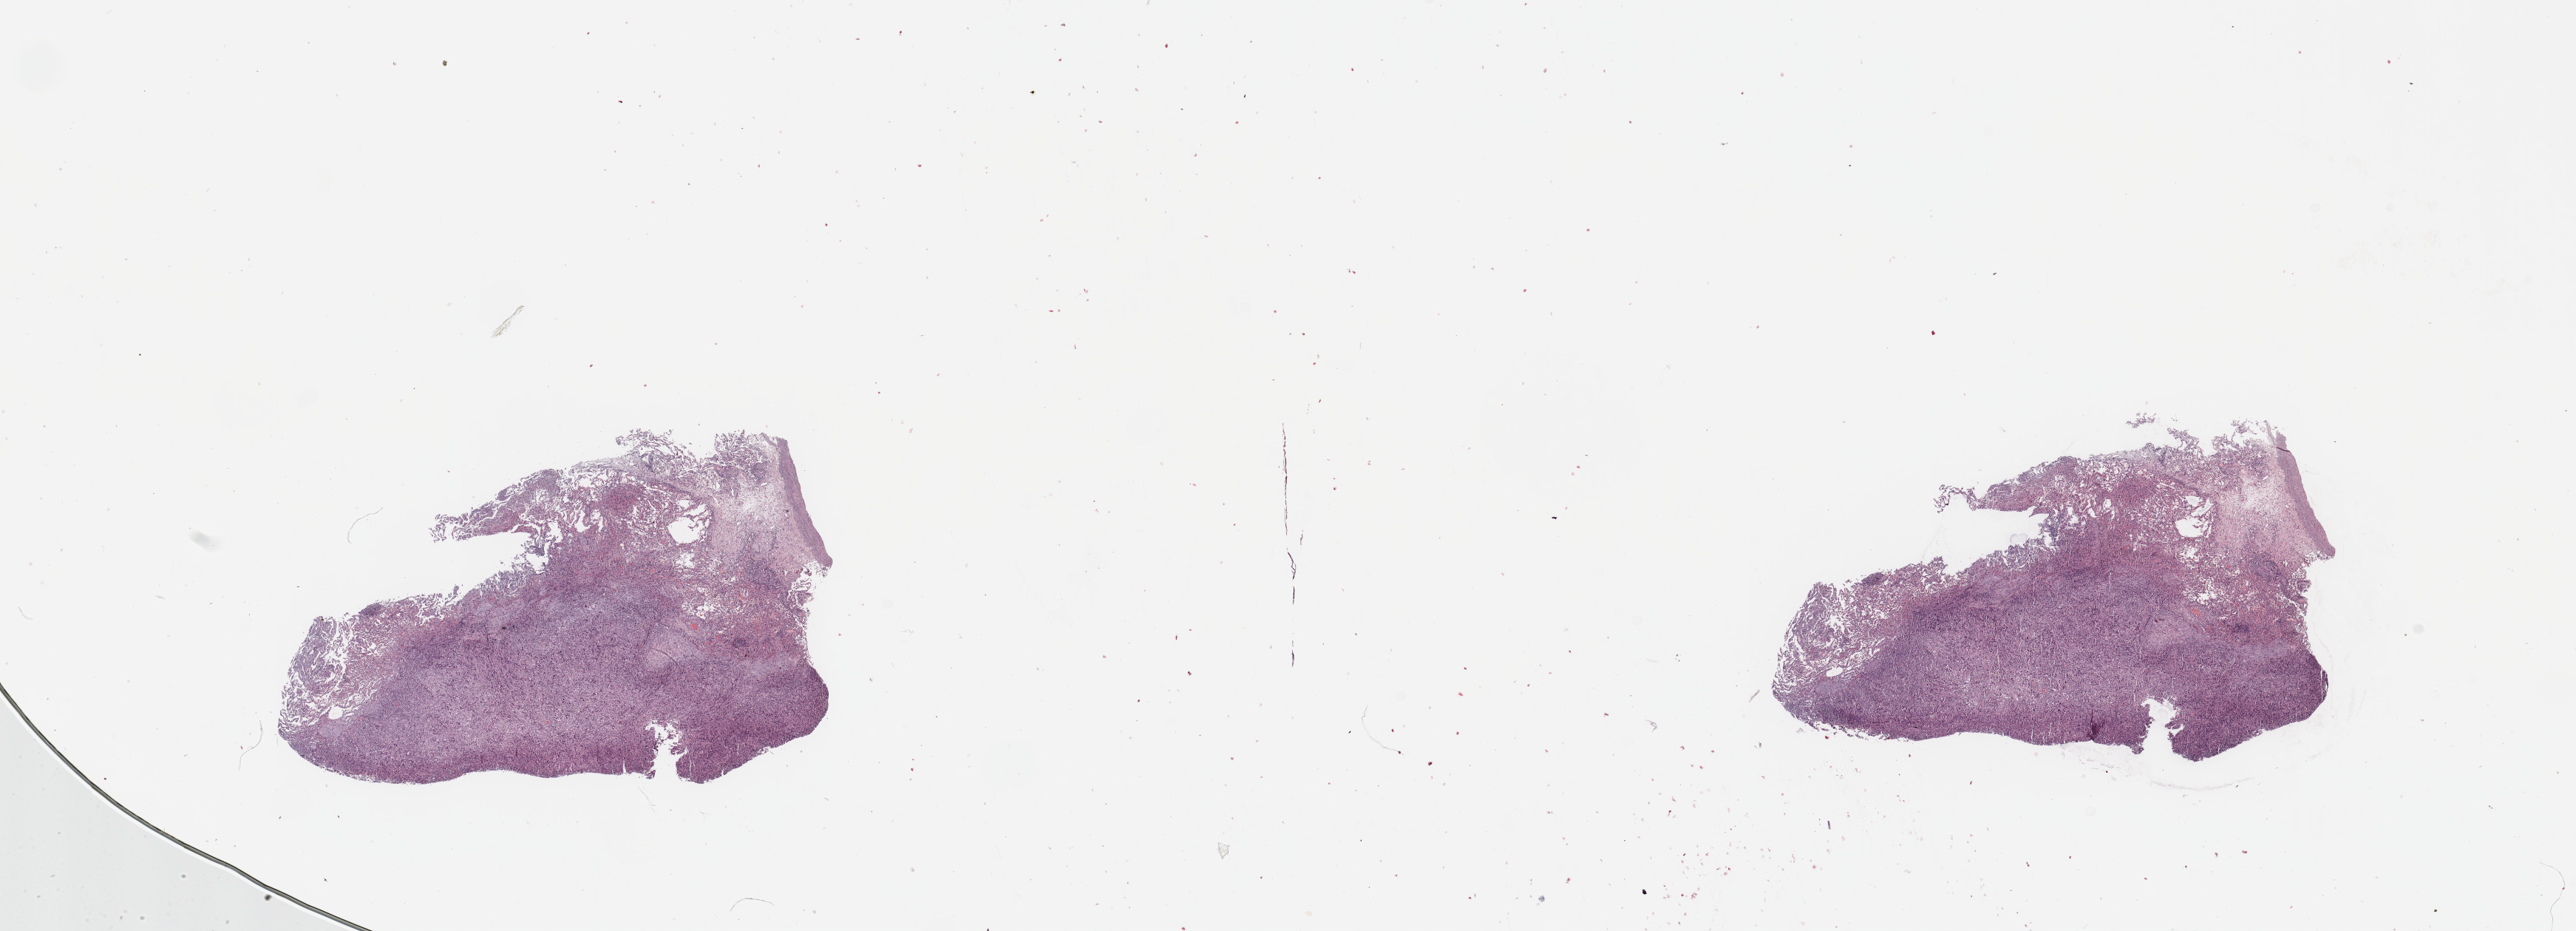
H&E-stained whole-slide image — shown as a low-resolution overview of the whole scanned area (about 27.6 x 10.0 mm), lung, tumour tissue. Male, 64 y/o. Histologic grade: G3 (poorly differentiated).
AJCC pathologic stage: IA1. Histologic diagnosis: Adenocarcinoma, NOS.